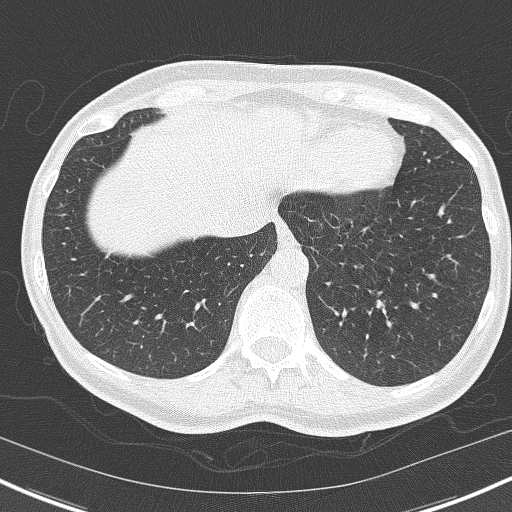
Low-dose screening chest CT, axial slice. Second screening round (one year after baseline). Lung window (W 1500 / L -600 HU). 2 mm slice thickness. 120 kVp. Slice 136 of 171 in the series. Female participant, aged 55 years at enrolment. Current smoker at enrolment.
Lesion marked by an expert reader, bounding box (x1, y1, x2, y2) in pixels: (360, 287, 402, 322). The exam's reader record, not a measurement of the box and not confirmed to be the same lesion: non-calcified nodule or mass ≥4 mm, right upper lobe, 13 × 6 mm, poorly defined margins, soft tissue attenuation, pre-existing on the prior screen: yes; interval growth: no. Note: the box lies in the patient's left hemithorax on this image, whereas the reader's record names the right lung; they may be different findings. Official screen result: positive, no significant change: stable abnormalities potentially related to lung cancer, unchanged since the prior screening exam. Participant outcome: lung cancer diagnosed 700 days after this screen — adenocarcinoma, NOS, left lower lobe, well differentiated (G1), stage IA (AJCC 6th edition), 11 mm at pathology.